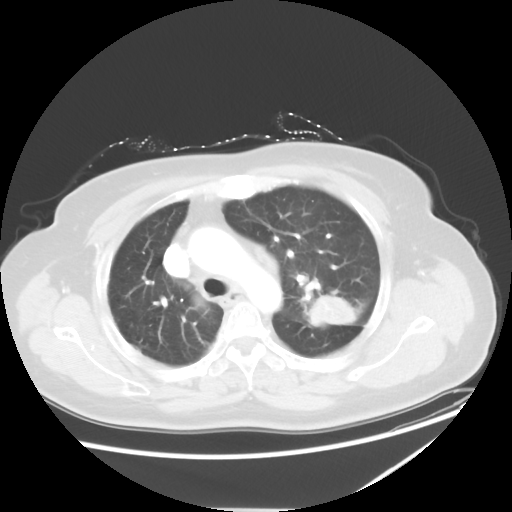
Chest CT, one axial slice. Position 39 of 54 along the scan axis. 120 kVp. Lung window (W 1500 / L -600 HU). 5 mm slice thickness. 512 × 512 image matrix, field of view 384 × 384 mm. Female patient, age 61 years. Case-level facts recorded for this patient, not image findings: clinical TNM (as recorded): T1c N3 M1.
Structures marked on this image (bounding box drawn by a radiologist):
- lung tumour (recorded histology: adenocarcinoma): box from (x=304, y=290) to (x=362, y=332) px